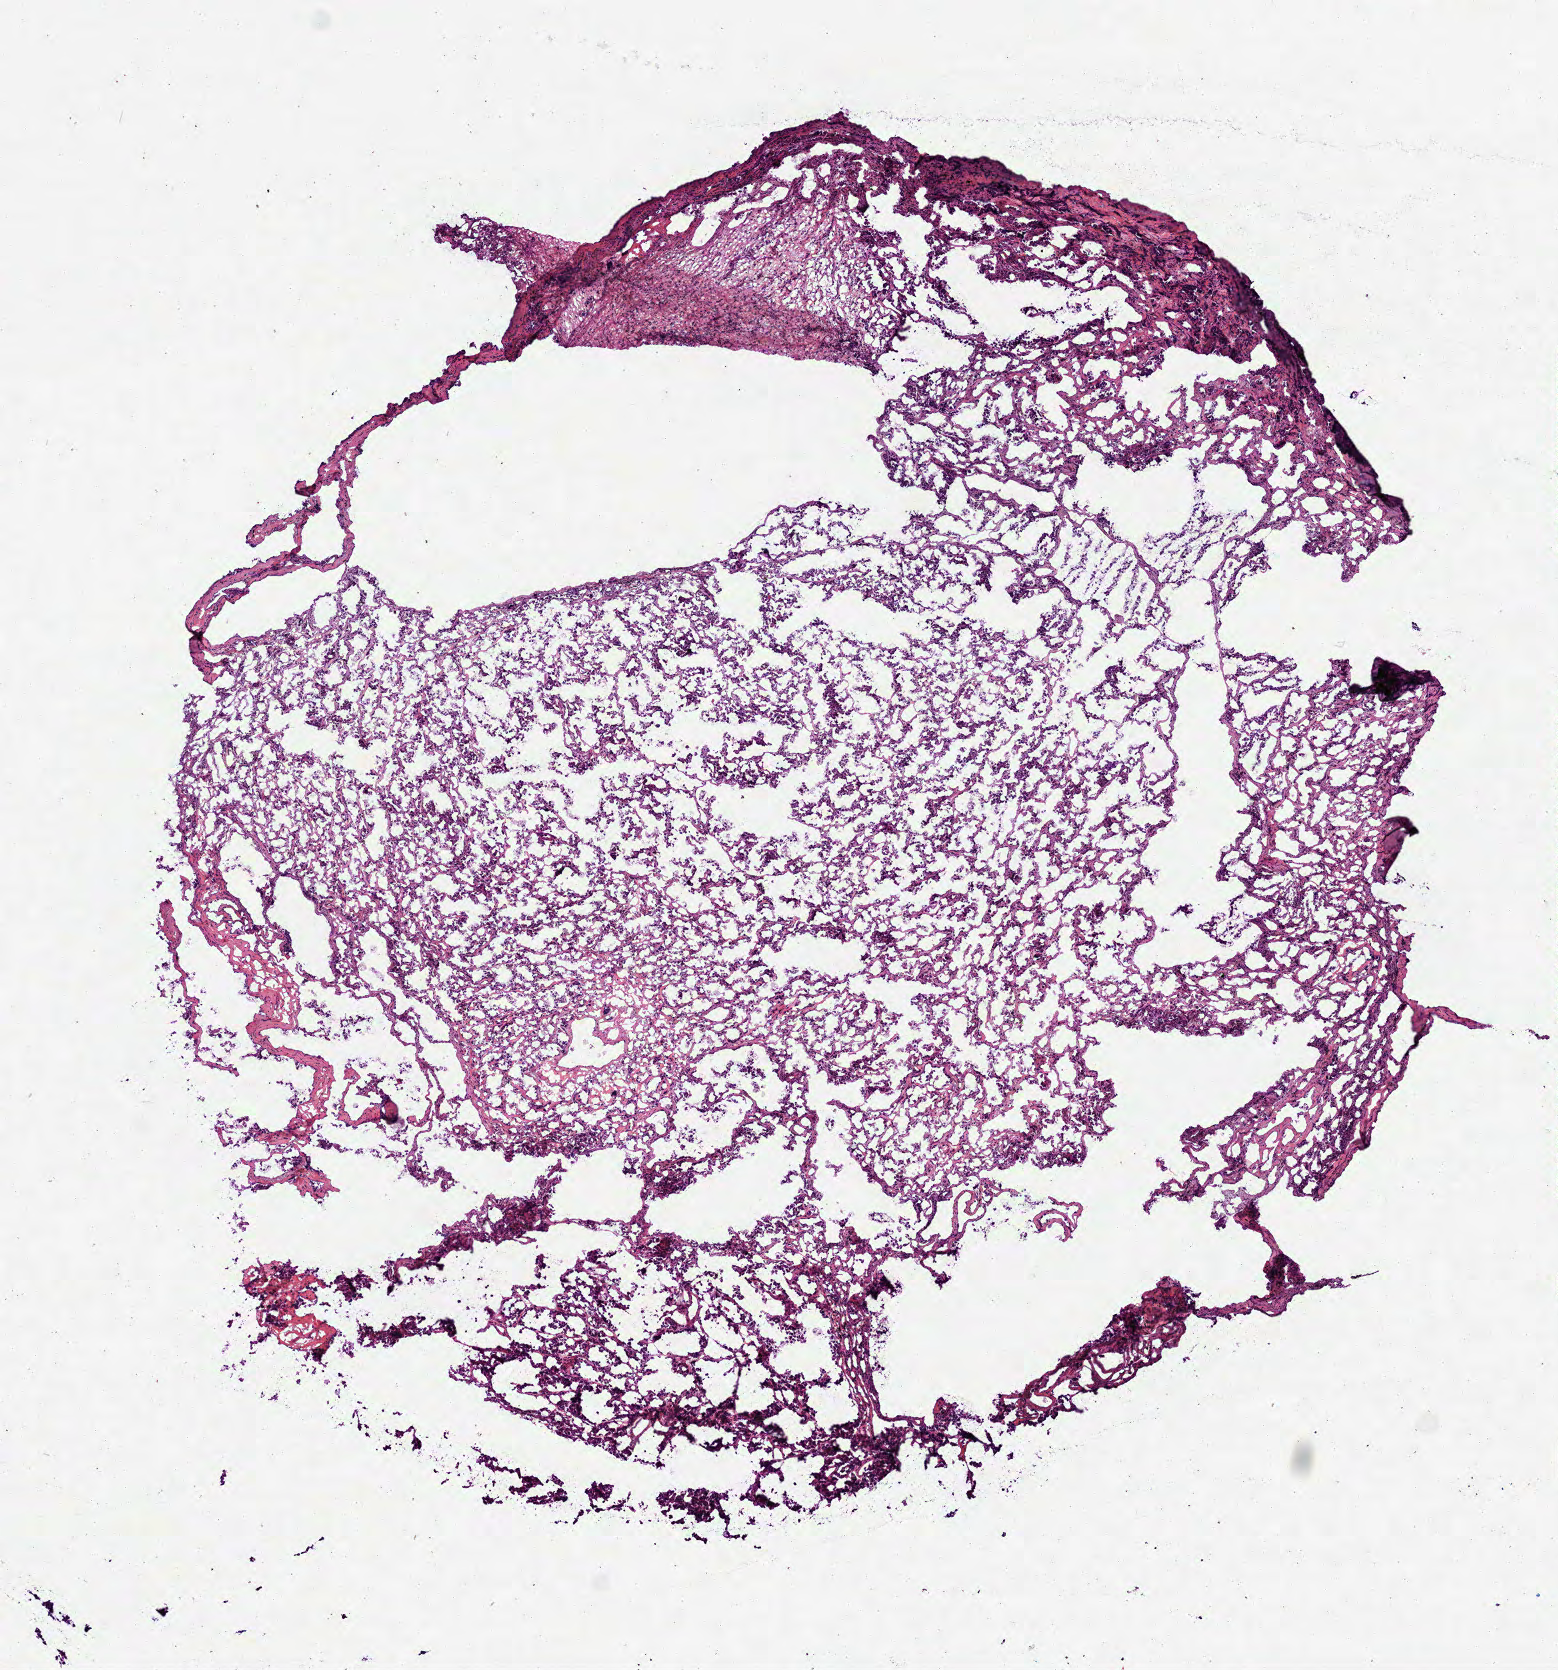
H&E whole-slide image, whole scanned area (about 6.3 x 6.7 mm) shown as a low-resolution overview; frozen section from the bottom of the tissue portion; sample: primary tumour, lung. Female patient; age at initial diagnosis 63 years.
Diagnosis: Adenocarcinoma with mixed subtypes (upper lobe, lung).